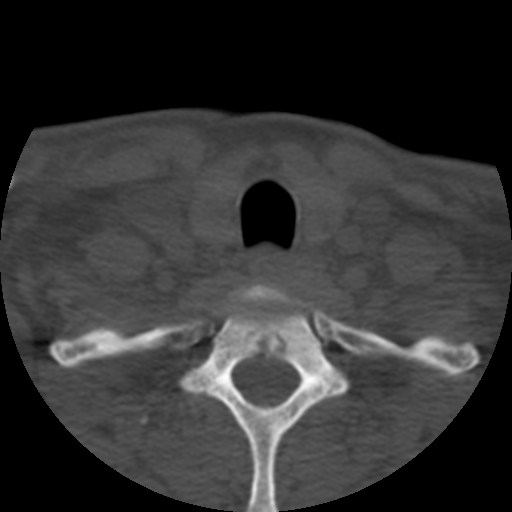
CT including the spine, one axial slice. Position 449 of 508 along the scan axis. Reconstruction kernel STANDARD. Bone window (W 1800 / L 400 HU). 512 × 512 image matrix. Patient age 57 years. From the clinical record (not read from this slice): primary cancer: prostate.
Annotated regions visible in this slice (semi-automatically segmented with operator editing):
- T1 vertebra: box from (x=140, y=285) to (x=347, y=512) px